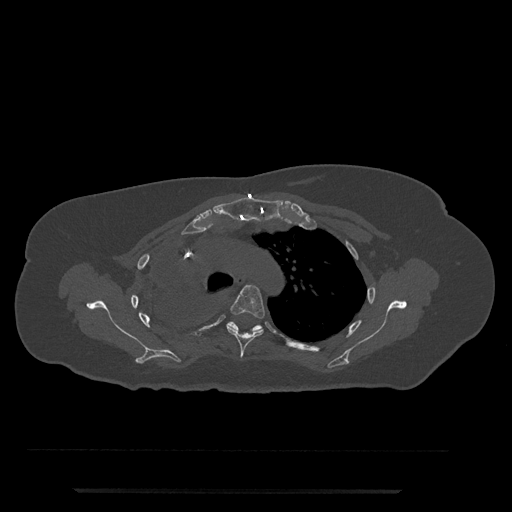
CT including the spine, one axial slice; reconstruction kernel Br40s/3; 120 kVp; bone window (W 1800 / L 400 HU); 0.5 mm slice thickness; 512 × 512 image matrix, field of view 440 × 440 mm. Patient: female, 51 years. From the clinical record (not read from this slice): primary cancer: neuro; vertebrae with lytic lesions (as recorded): T8.
Annotated regions visible in this slice (semi-automatic segmentation, software-assisted and operator-edited):
- T4 vertebra: bounding box (x1, y1, x2, y2) in pixels: (227, 285, 265, 358)
- T5 vertebra: (227, 321, 263, 333)